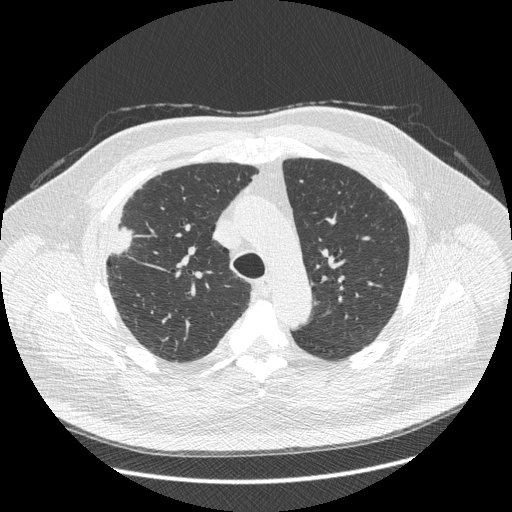
Low-dose screening chest CT, one axial slice. Reconstruction kernel STANDARD. Lung window (W 1500 / L -600 HU). 512 × 512 image matrix, field of view 400 × 400 mm.
Structures marked on this image (outlined manually by an expert reader):
- lesion 1 (tumor, upper lobe of right lung): bounding box <112,228,133,254> (left, top, right, bottom; pixels)